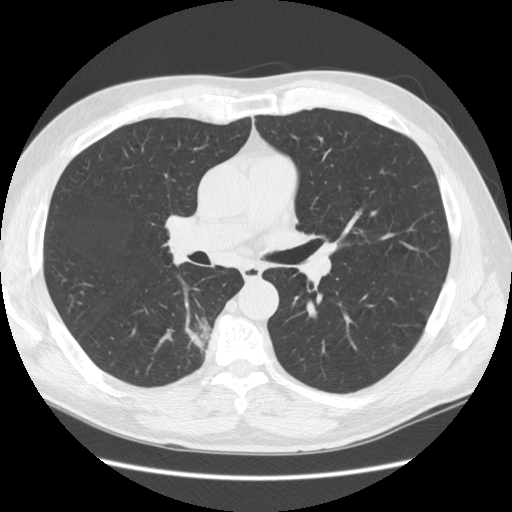
Axial slice from a low-dose chest CT screening exam, second annual screen, lung window (W 1500 / L -600 HU), slice 59 of 133 in the series, 512 × 512 image matrix, field of view 370 × 370 mm. Male, age 69 years at enrolment.
- Lesion marked by an expert reader, box from (x=169, y=306) to (x=225, y=359) px.
- The screening reader recorded 2 non-calcified nodules or masses ≥4 mm on this exam; which of them this box marks is not recorded.
- Official screen result: positive, other.
- Lung cancer was diagnosed 88 days after this screen: bronchiolo-alveolar adenocarcinoma, NOS, right lower lobe, well differentiated (G1), stage IB (AJCC 6th edition), 23 mm at pathology.